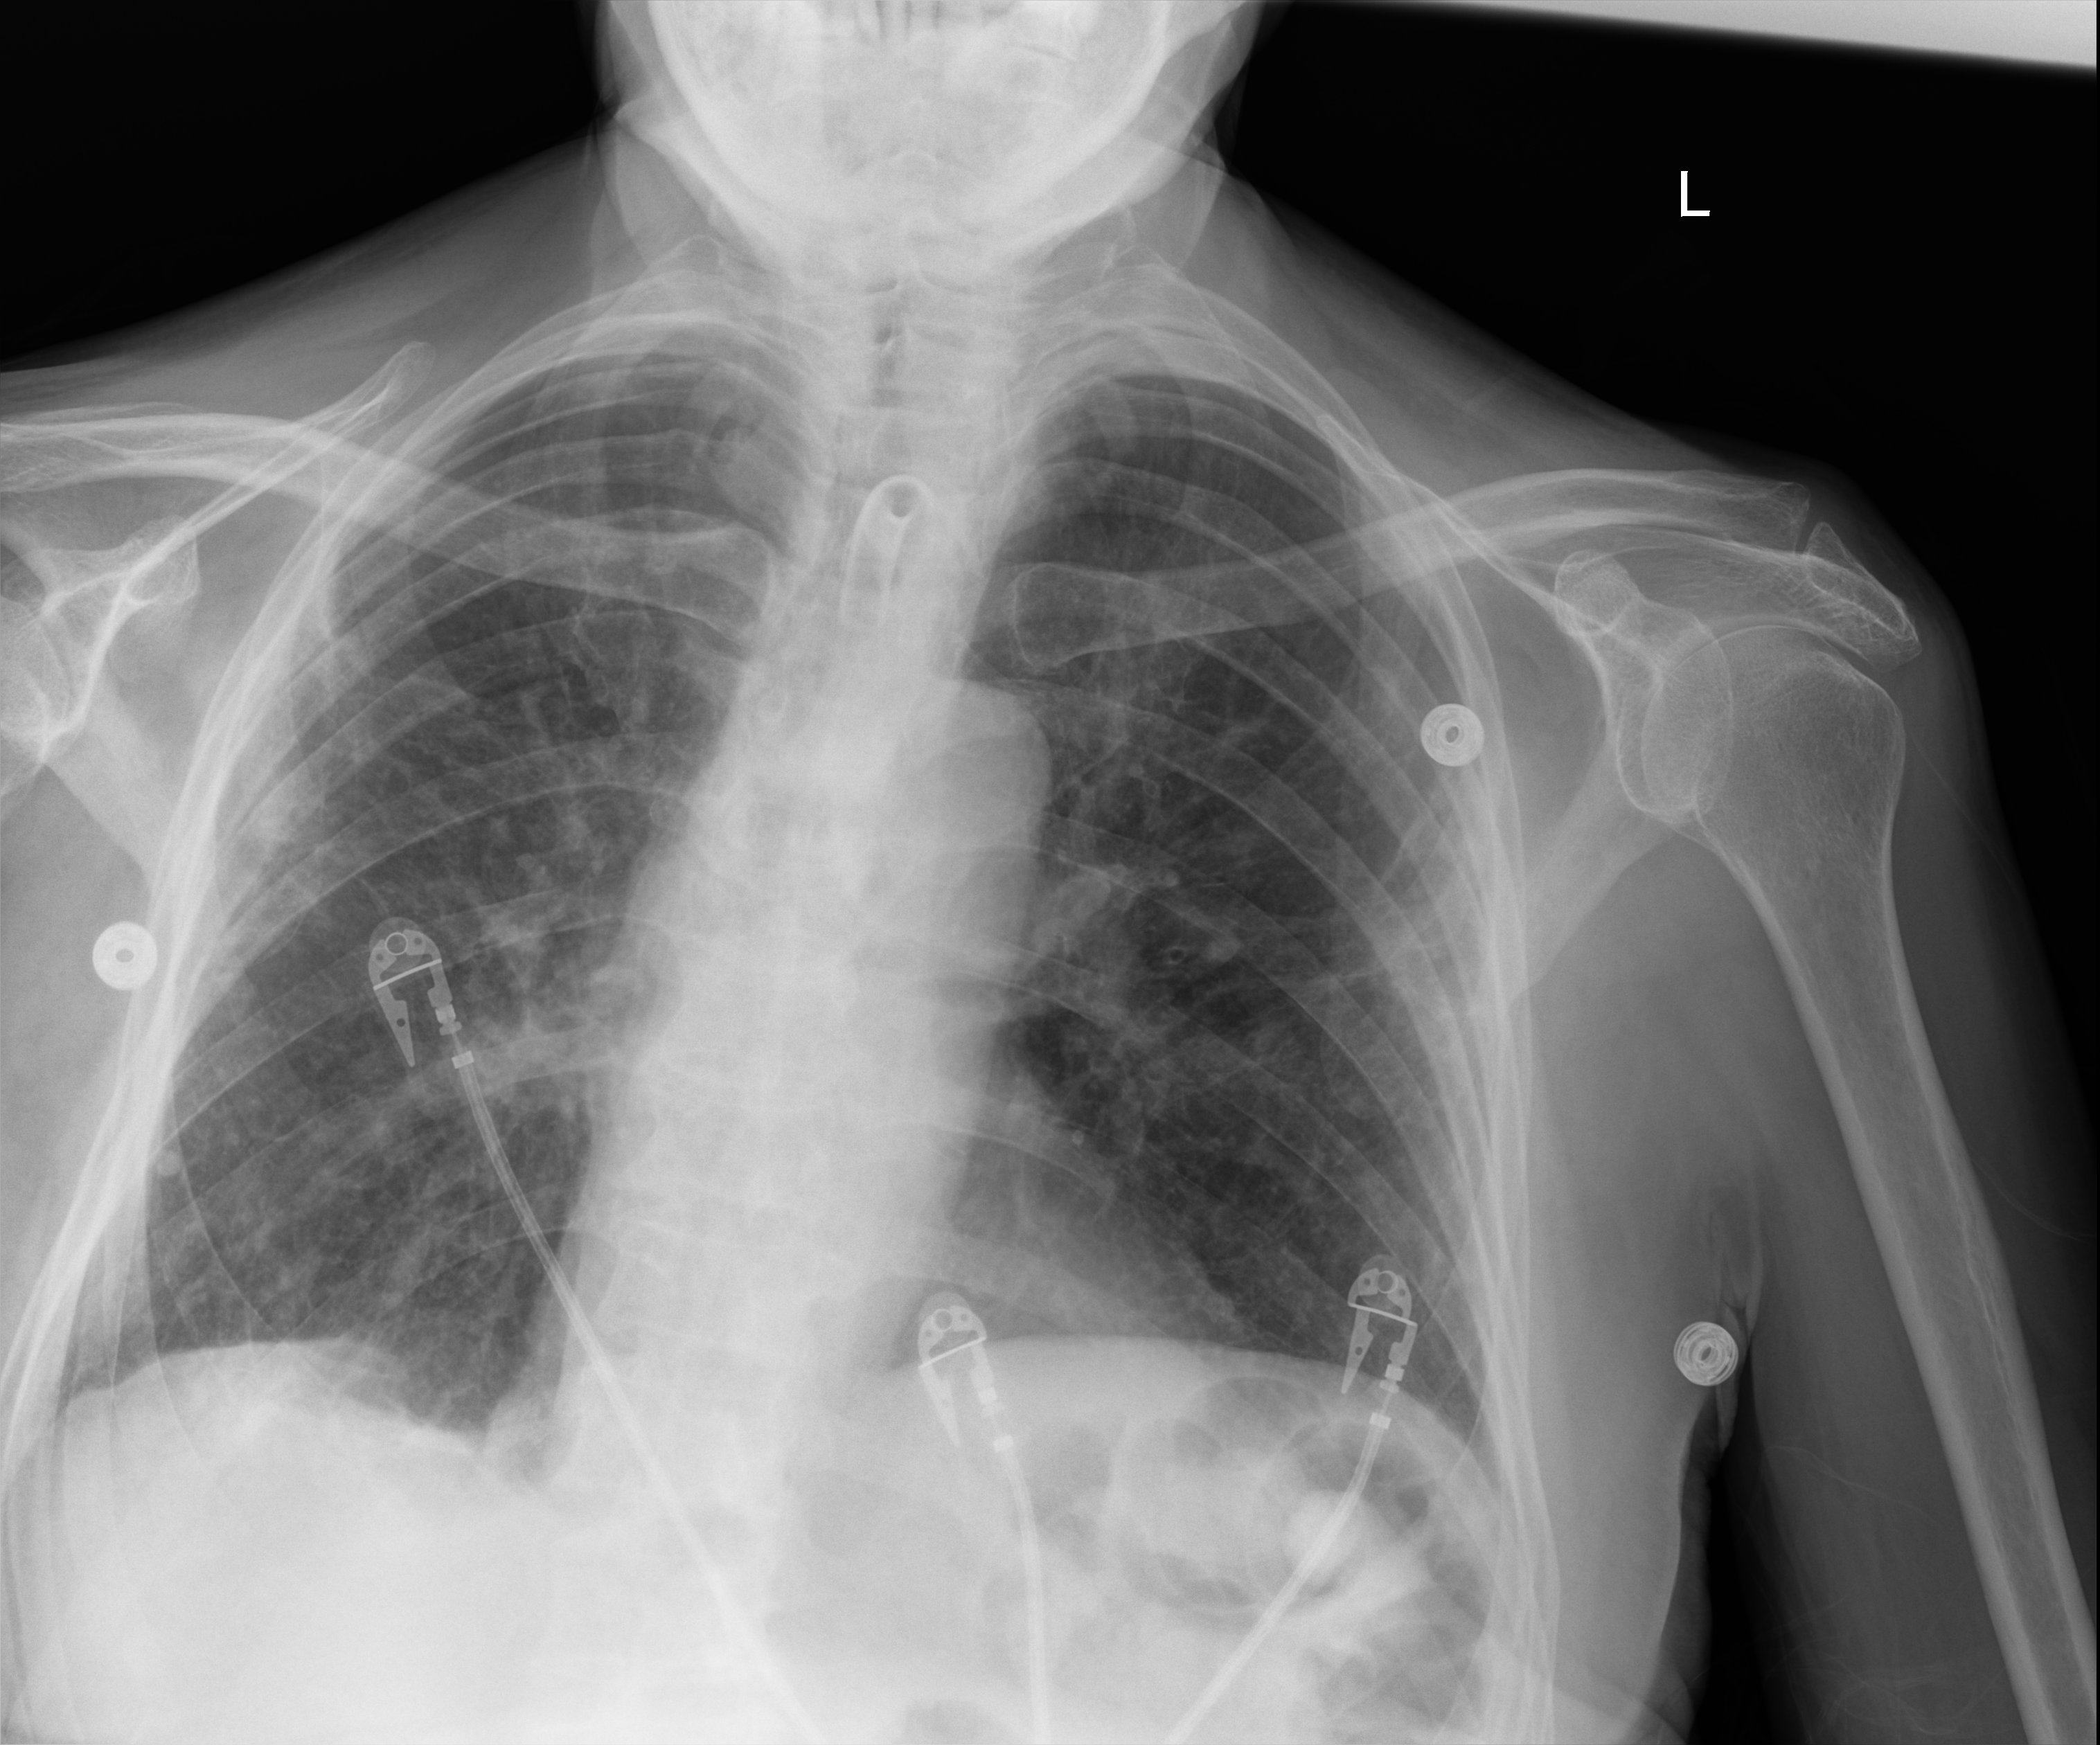
Chest X-ray (portable). Male patient hospitalised with COVID-19, age 75–90 years.
Hospital-stay facts (about this admission, not read from this image; timing relative to this image not recorded):
- mechanically ventilated during this hospital stay: yes
- COPD (admission record): no